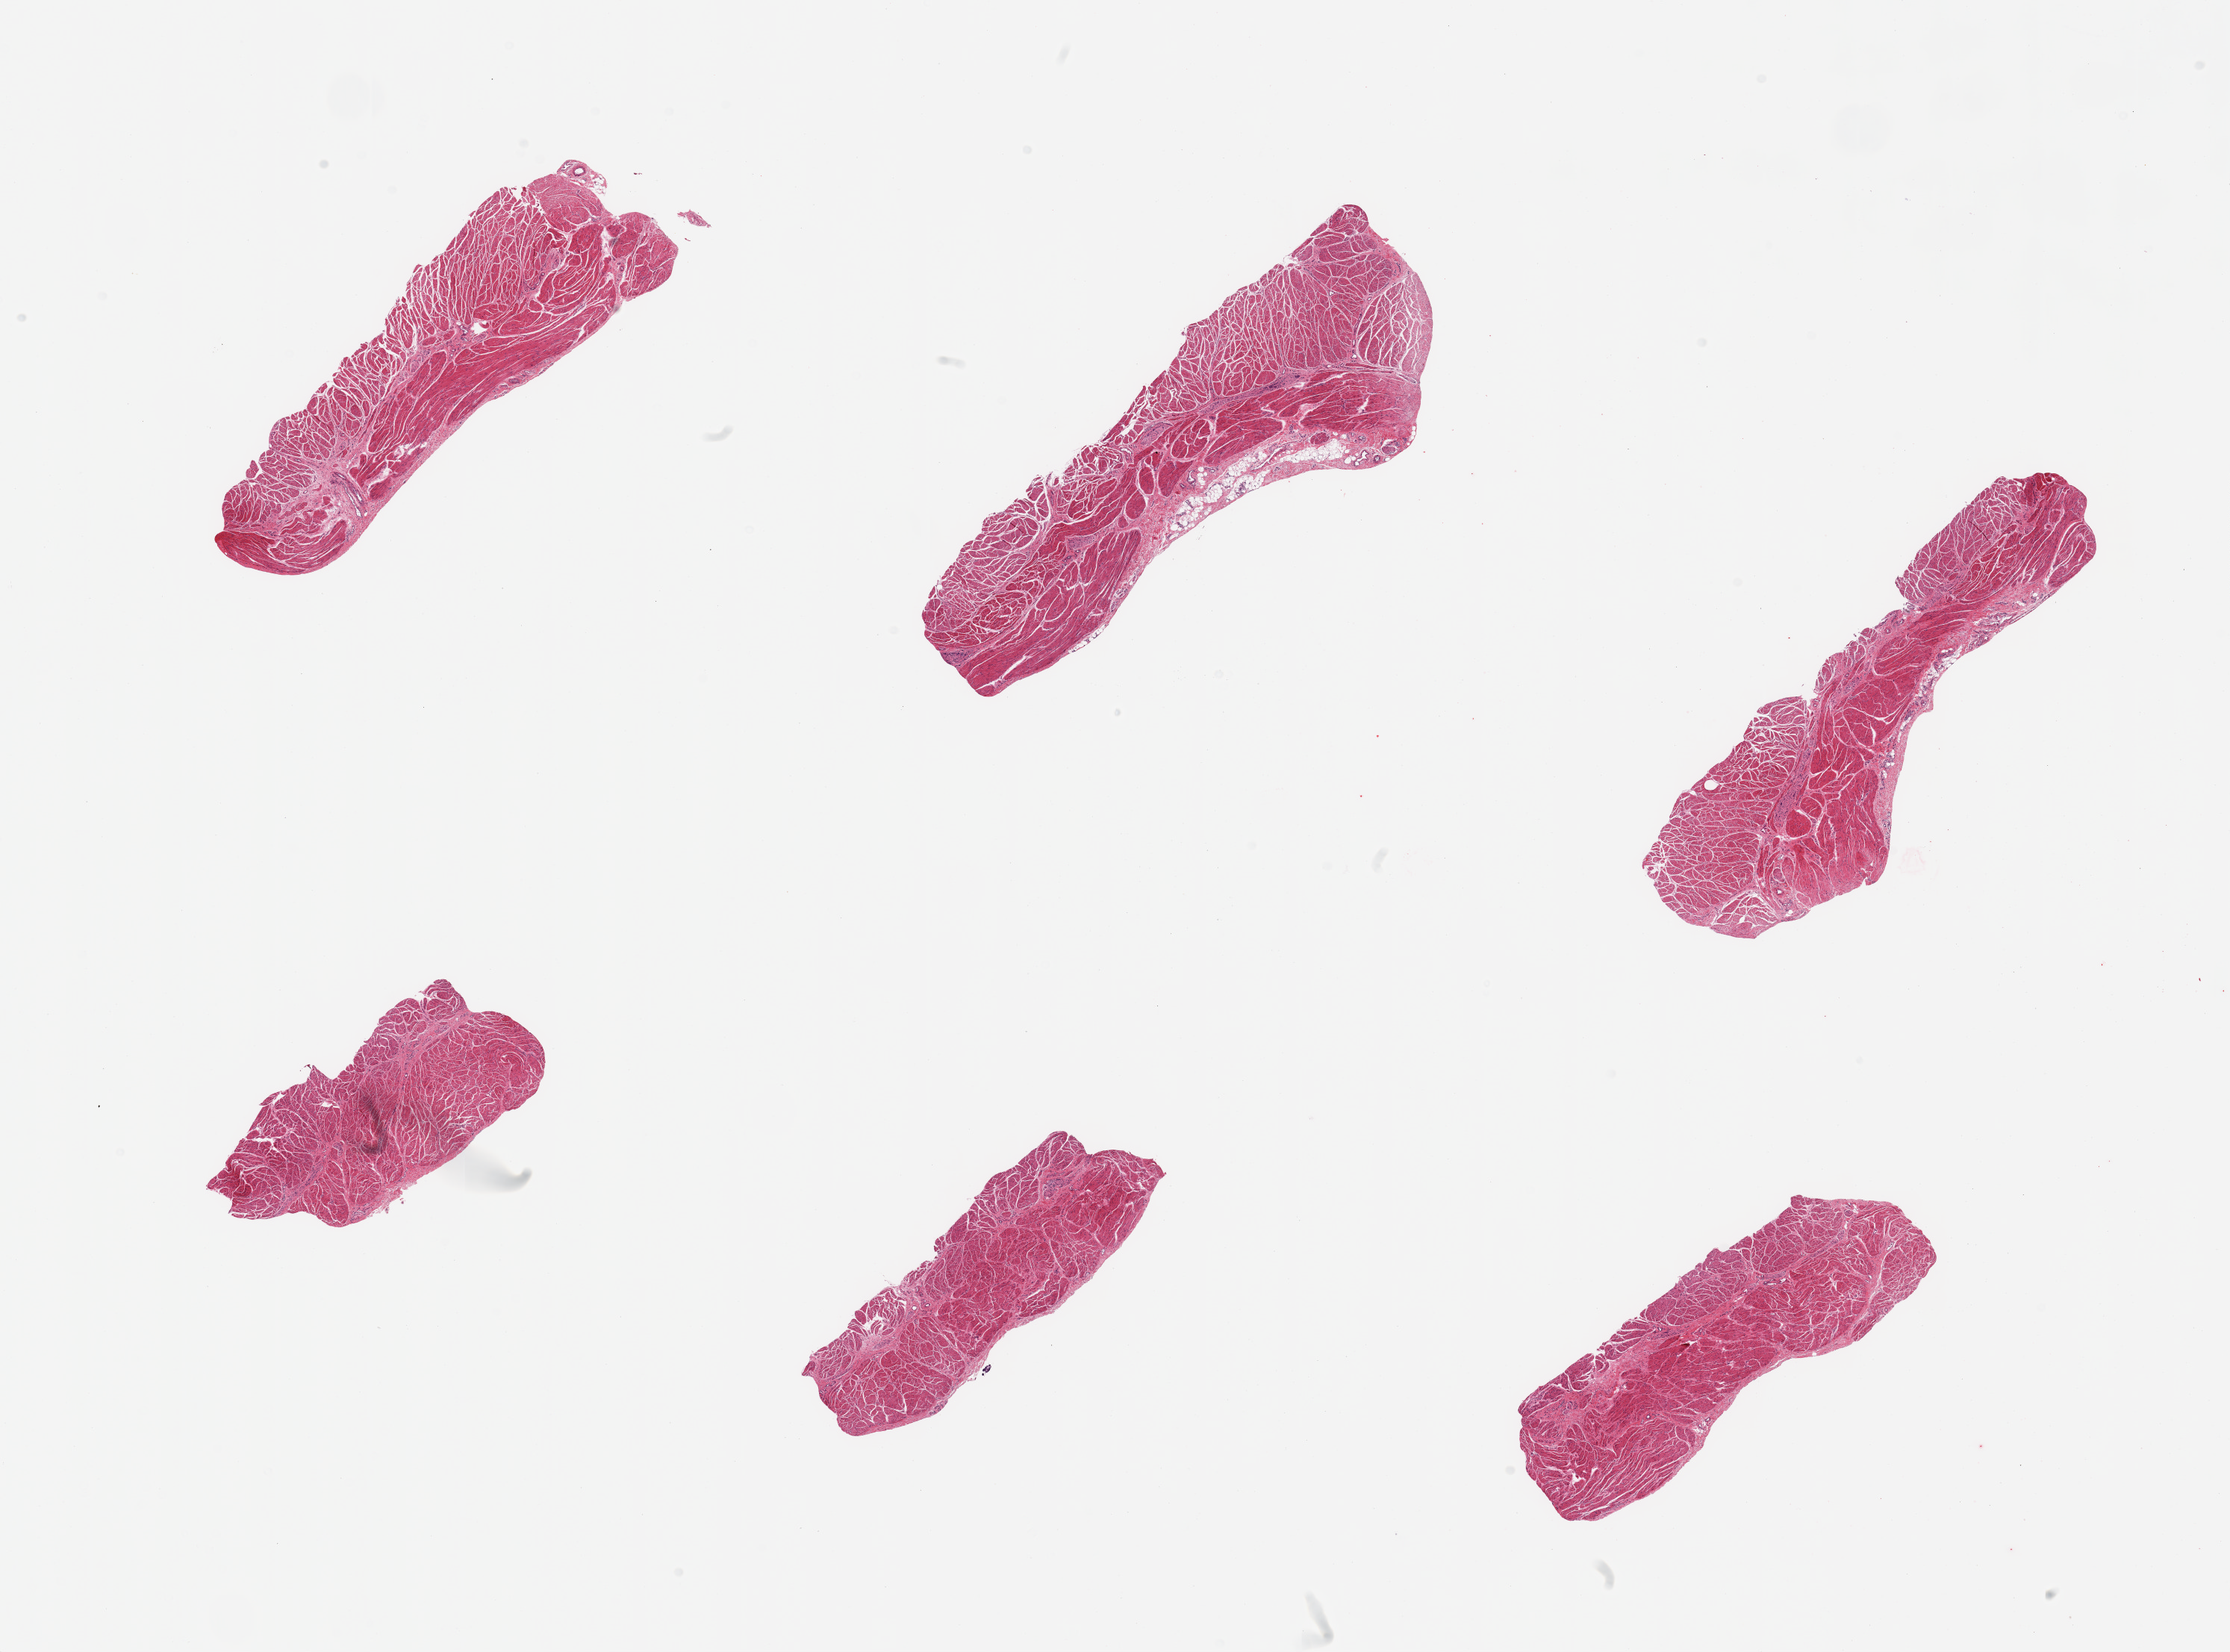
Hematoxylin and eosin (H&E) whole-slide image — a low-resolution overview of the entire scanned area, about 23.6 x 17.5 mm (acquisition: 20x scan), PAXgene-fixed paraffin-embedded (PFPE) section, target tissue: gastroesophageal junction, donor tissue sample. Donor sex: male.
Pathologist's review note for this sample: 6 pieces, confirmed target muscularis.